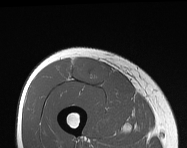
MRI of an extremity soft-tissue mass, one axial slice. Slice 55 of 114 in the series (ordered by position). MR volume resampled by the dataset authors to the PET/CT grid (not the native acquisition matrix). 3.27 mm slice thickness. 187 × 148 image matrix. Male patient. Case-level facts recorded for this patient, not image findings: histological type: pleiomorphic leiomyosarcoma; grade: intermediate; site of the primary tumour: right thigh.
Annotated regions visible in this slice (expert contour drawn on MRI and transferred to this co-registered scan by the dataset authors):
- gross tumour volume including surrounding oedema: bounding box (x1, y1, x2, y2) in pixels: (72, 58, 110, 87)